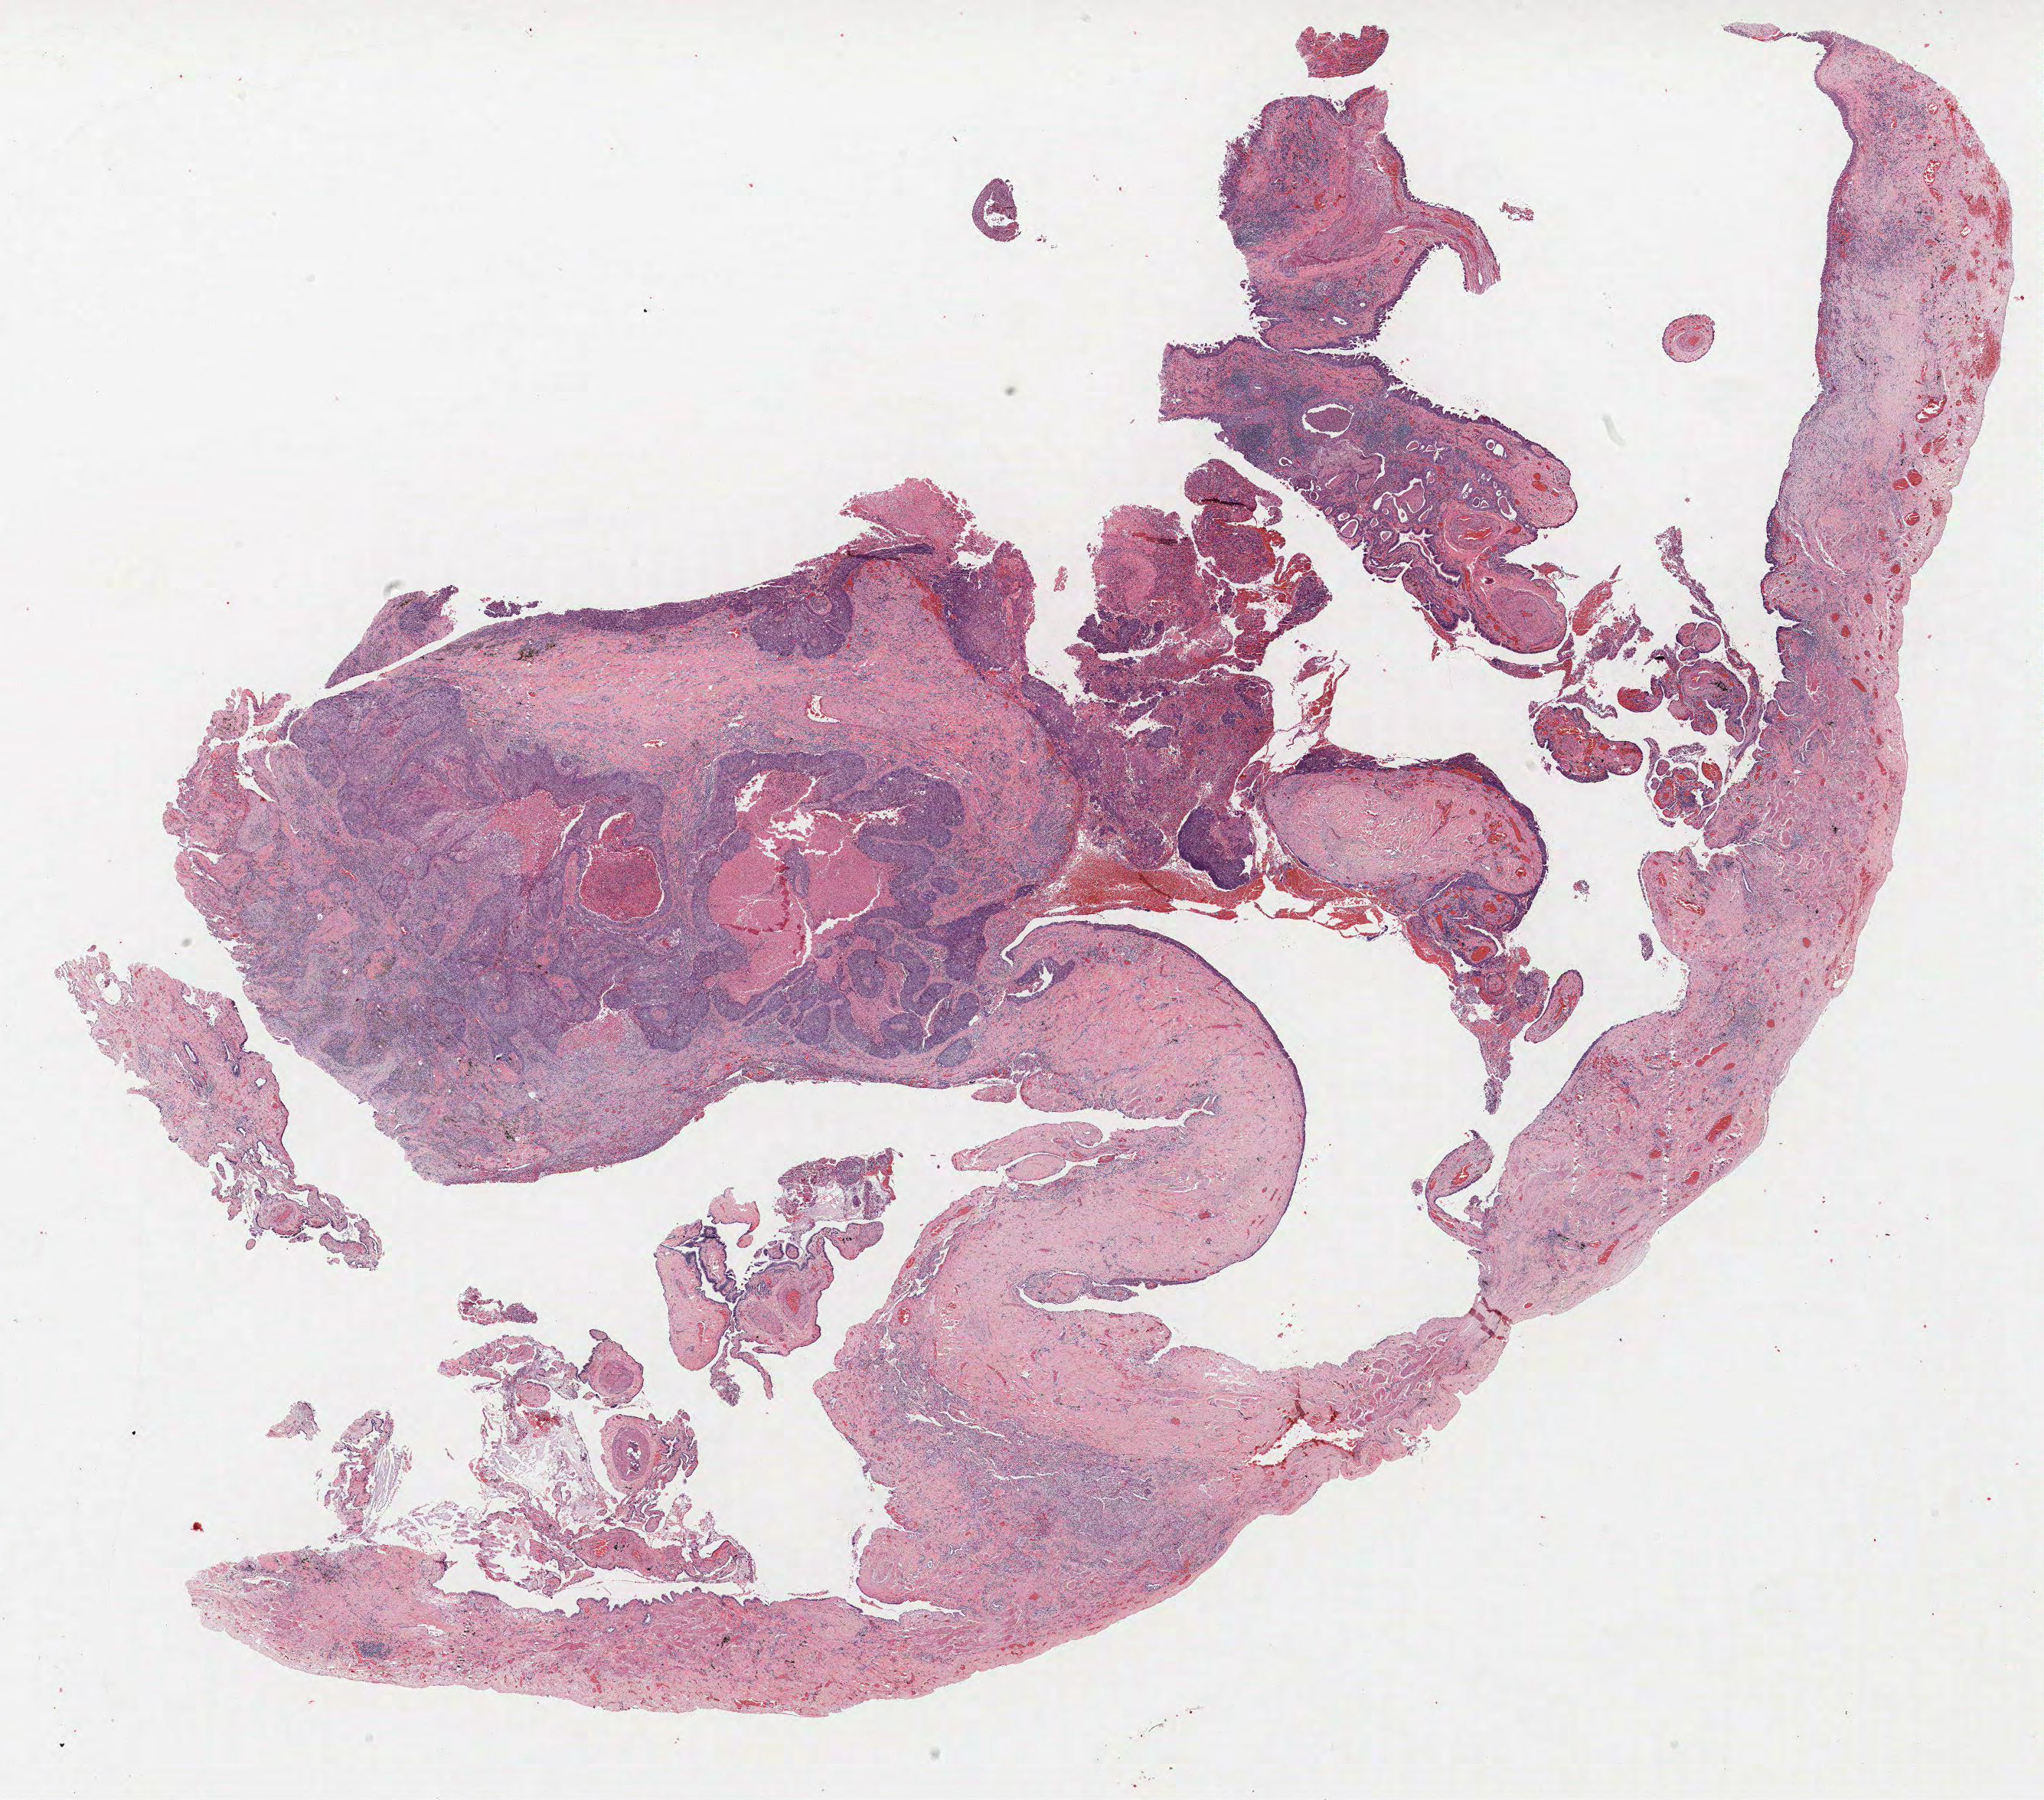
H&E whole-slide image, low-resolution overview of the scanned area, about 21.4 x 18.8 mm (slide scanned at 40x). FFPE section. Lung. Male, age 58 at enrolment. Current smoker at enrolment. Grade: moderately differentiated (G2).
Stage (AJCC 6th edition): IB. Primary tumour location (clinical record): right lower lobe. Participant's lung-cancer diagnosis: Squamous cell carcinoma, keratinizing, NOS. Tumour size (pathology): 38 mm. Note: participant had 2 primary lung cancers recorded; fields above describe the first.